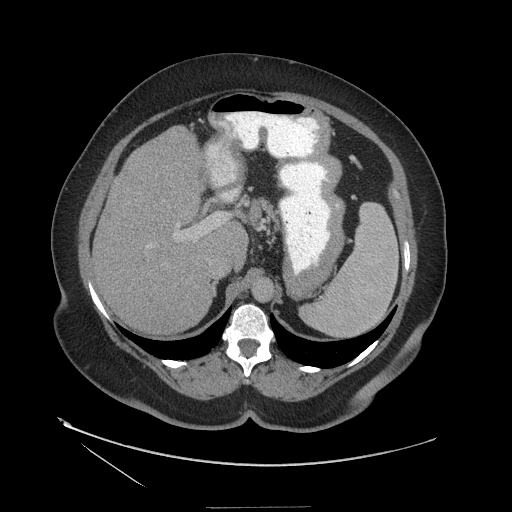
Contrast-enhanced abdominal CT (liver protocol), one axial slice. Position 77 of 127 along the scan axis. Reconstruction kernel STANDARD. Soft-tissue window (W 400 / L 40 HU). 512 × 512 image matrix. From the clinical record (not read from this slice): diagnosis: hepatocellular carcinoma (patient treated with transarterial chemoembolisation; whether this scan precedes or follows treatment is not stated here); TNM stage (as recorded): Stage-II; Child-Pugh class: A; tumour differentiation: well differentiated; tumour nodularity: multinodular.
Outlined on this slice (semi-automatic segmentation, software-assisted and operator-edited):
- liver parenchyma outside the tumour (the mass and vessels are separate outlines, so this box may not span the whole liver): box from (x=92, y=126) to (x=248, y=334) px
- liver vessels: (x=150, y=158)–(x=235, y=246)